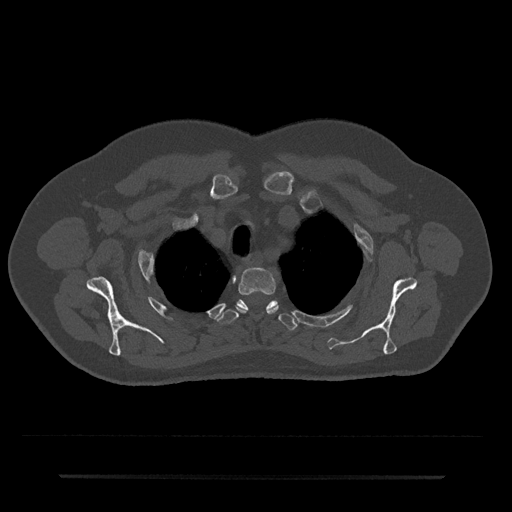
CT including the spine, one axial slice. Slice 588 of 797 in the series (ordered by position). Reconstruction kernel Br40s/3. 120 kVp. Bone window (W 1800 / L 400 HU). 0.5 mm slice thickness. 512 × 512 image matrix, field of view 437 × 437 mm. Male patient, age 69 years. From the clinical record (not read from this slice): primary cancer: prostate.
Annotated regions visible in this slice (semi-automatic segmentation, software-assisted and operator-edited):
- T2 vertebra: bounding box (x1, y1, x2, y2) in pixels: (237, 268, 278, 314)
- T3 vertebra: (217, 299, 297, 330)